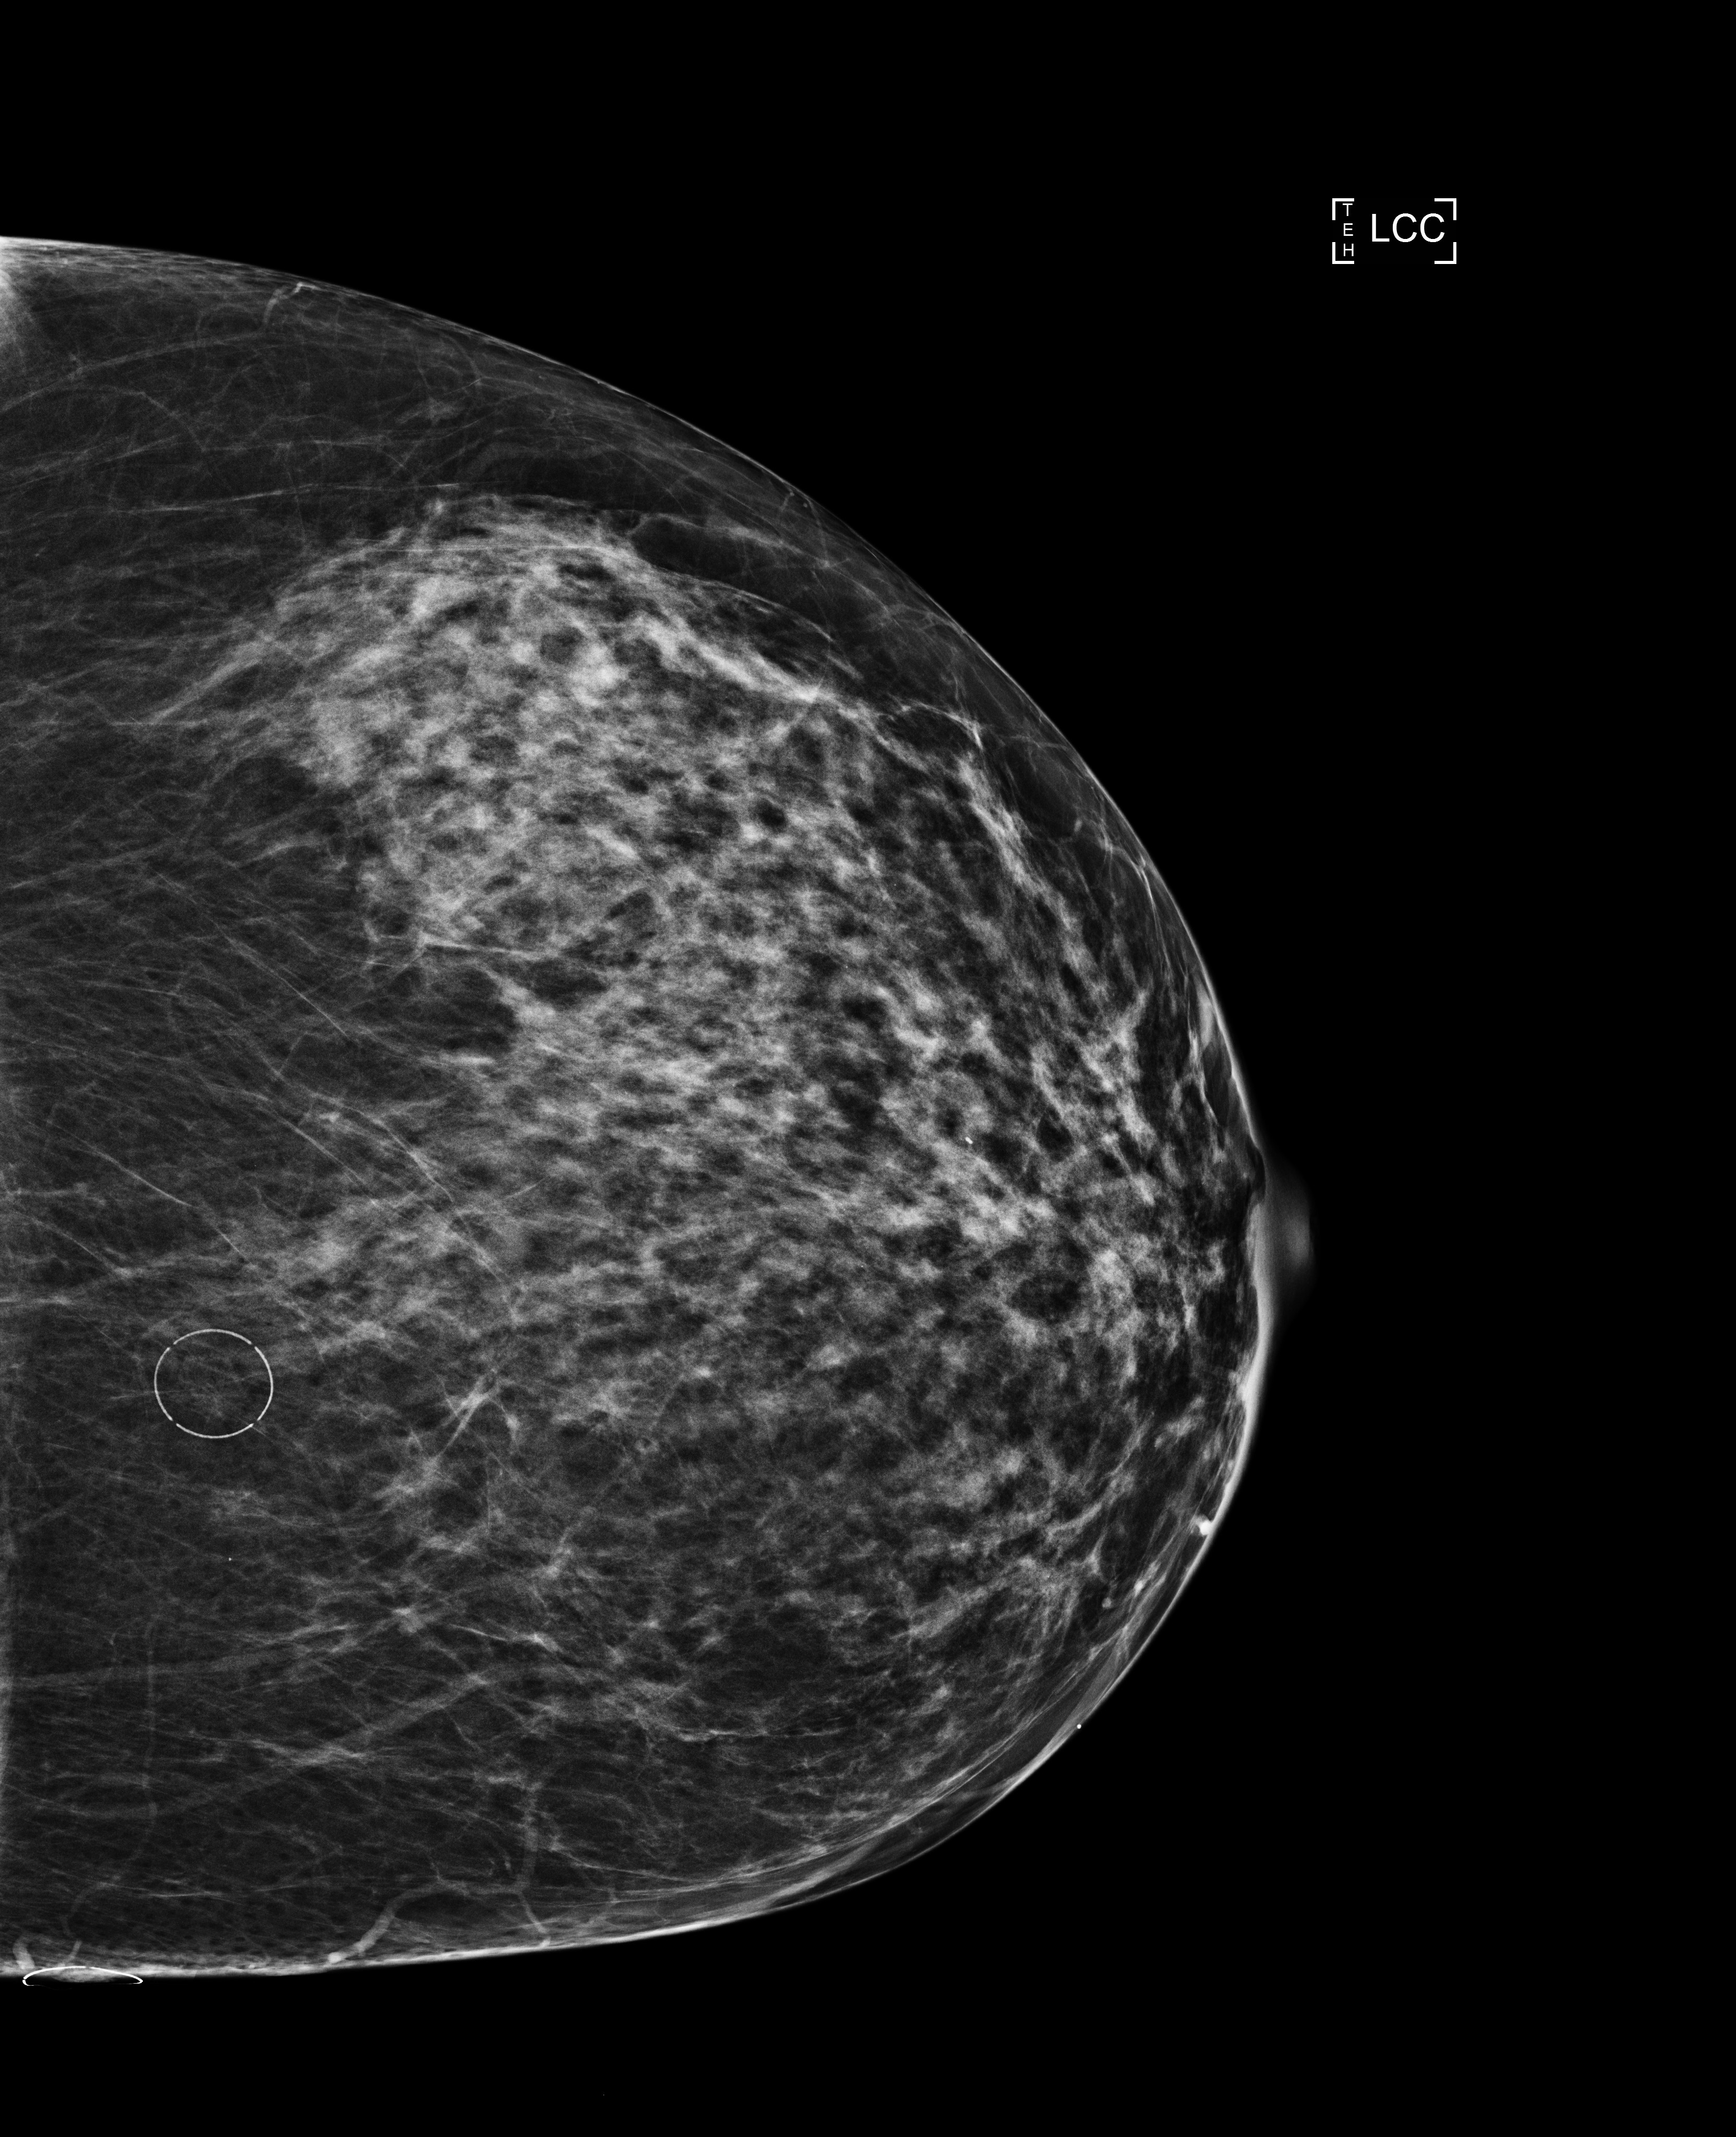
Screening examination, system: Selenia Dimensions. Patient aged 61 years (female).
Image type: full-field digital mammogram. Breast: left. Projection: CC view. BI-RADS breast density category at the screening exam (both breasts, scale 1–4): 3. Final BI-RADS category for the screening round (tomosynthesis exam, both breasts): category 2. Recall: recalled for additional imaging after this screen.